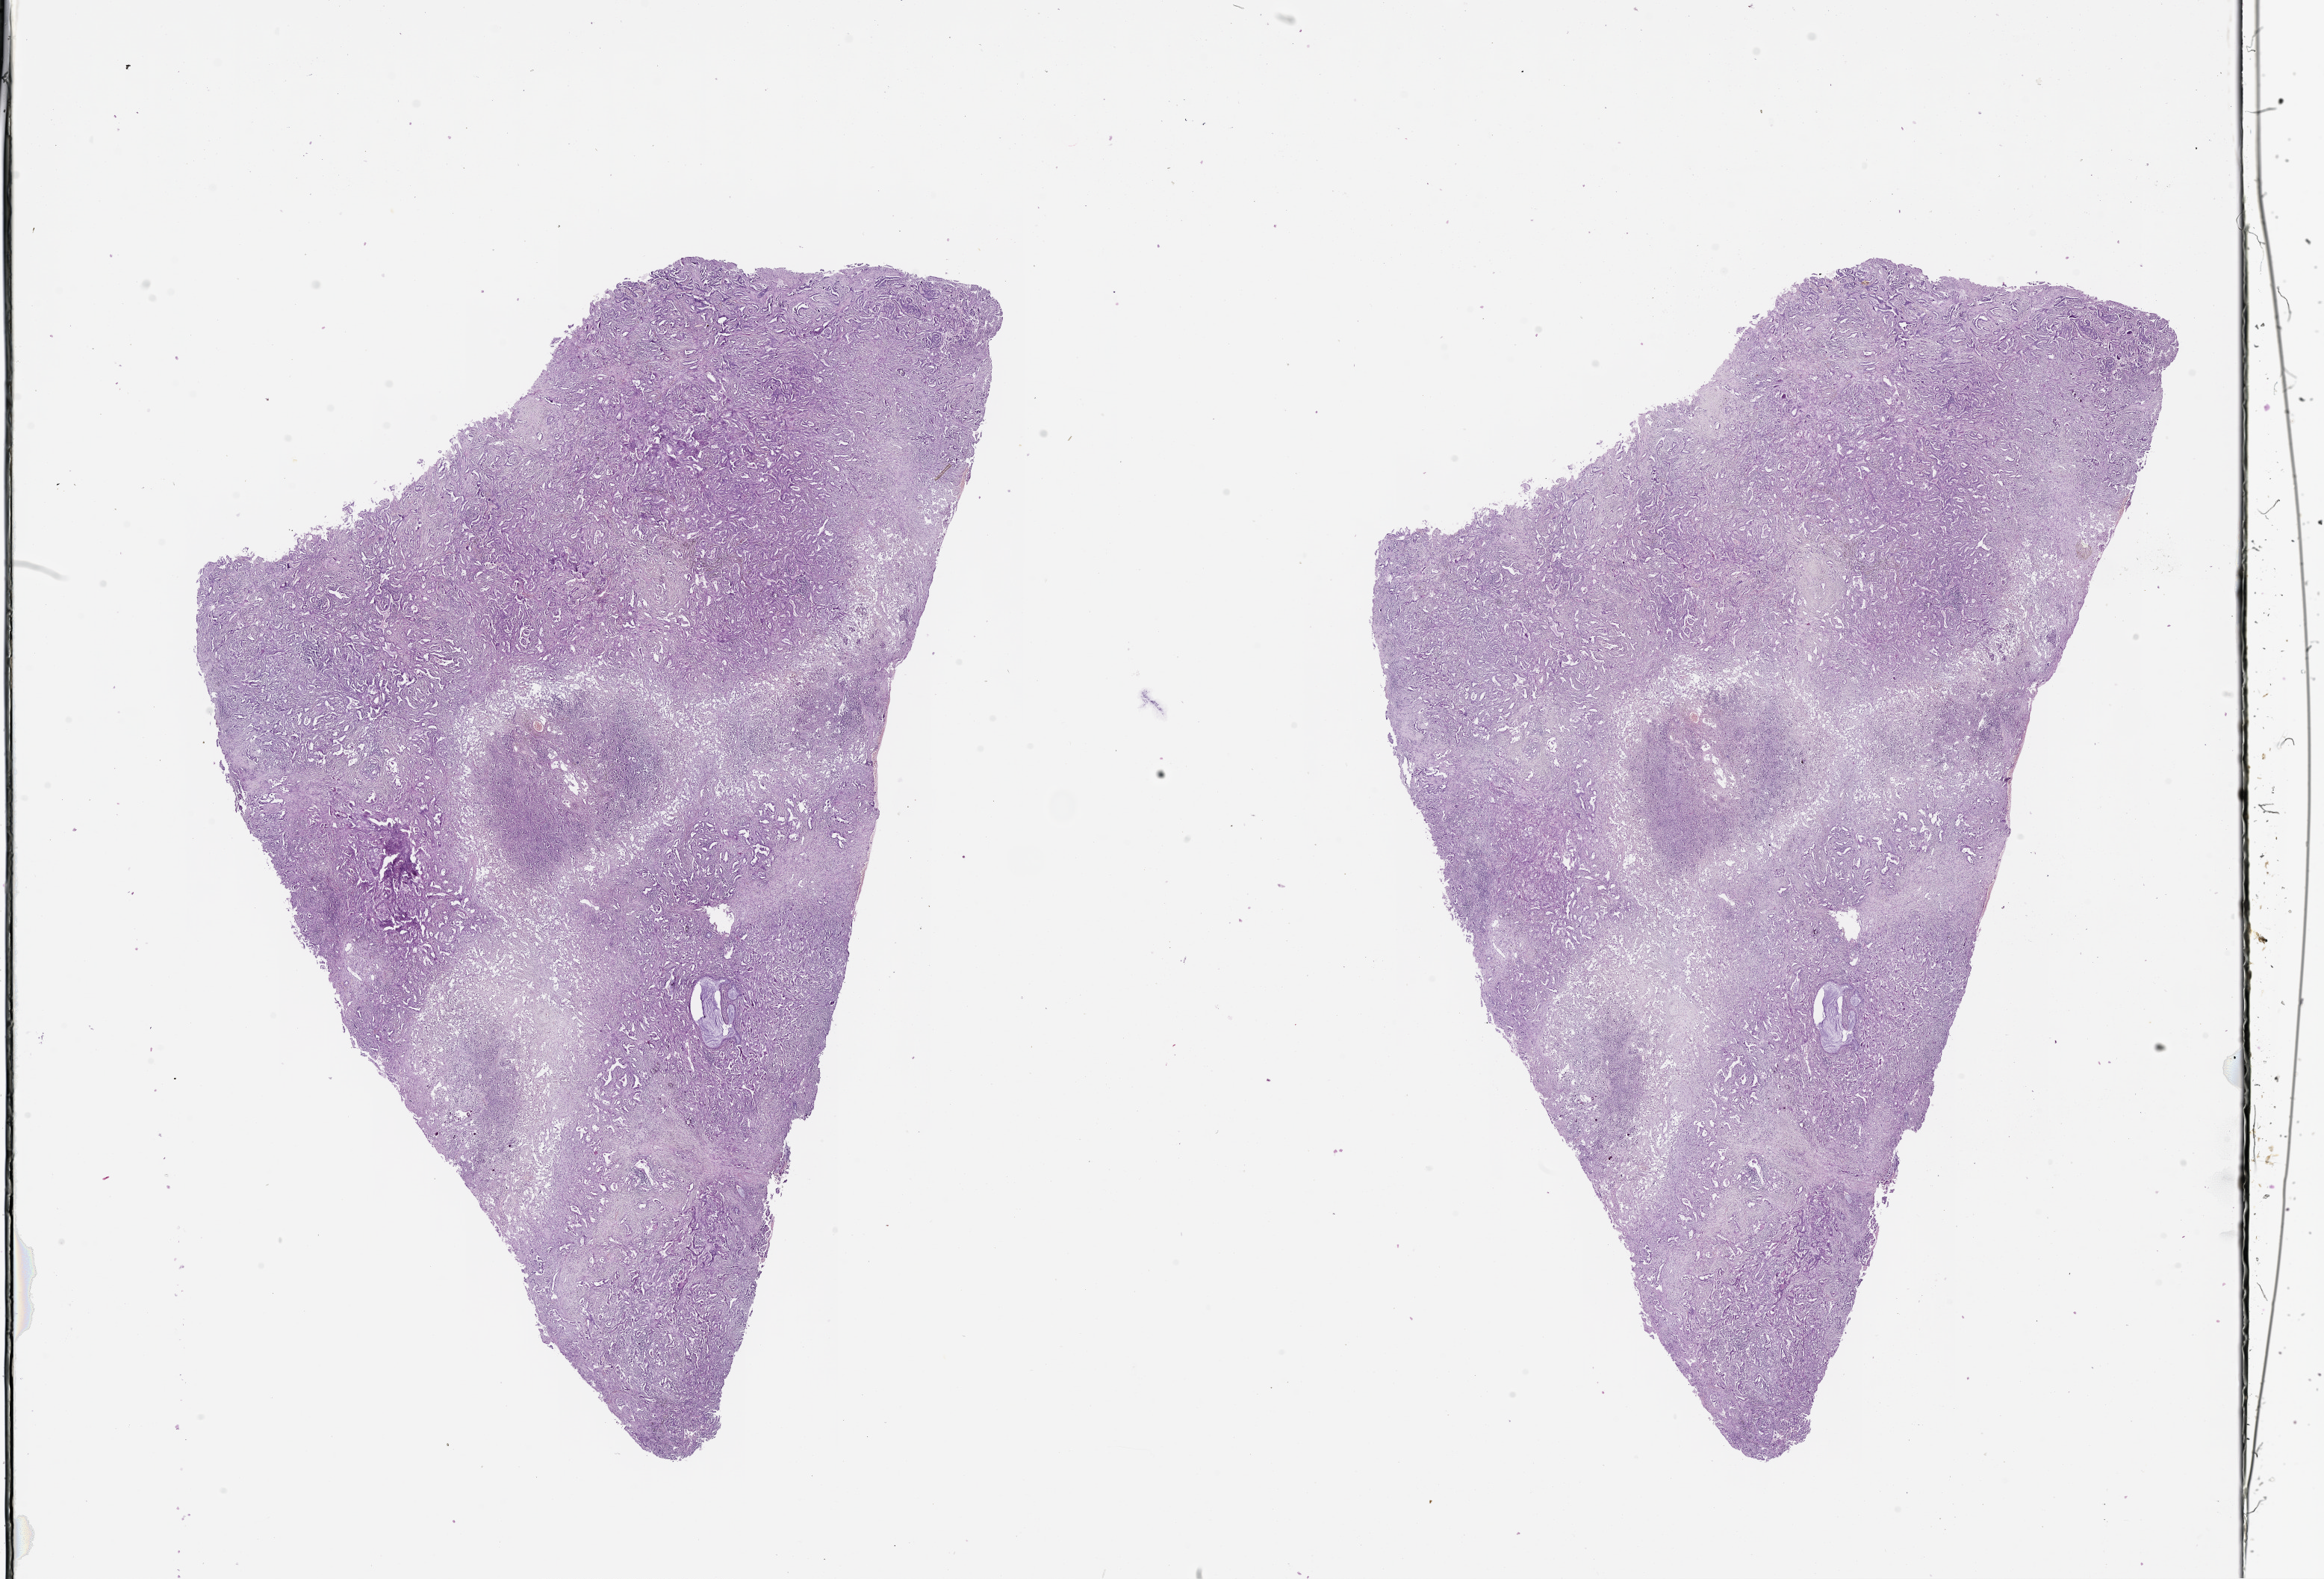
Whole-slide histology image, H&E-stained — shown as a low-resolution overview of the whole scanned area (about 25.1 x 17.0 mm), lung, tumour tissue. 61-year-old male patient. Histologic grade: G2 (moderately differentiated).
Diagnosis: Adenocarcinoma, NOS. AJCC pathologic stage: IIIA. Primary tumour site (as recorded): right upper lobe.